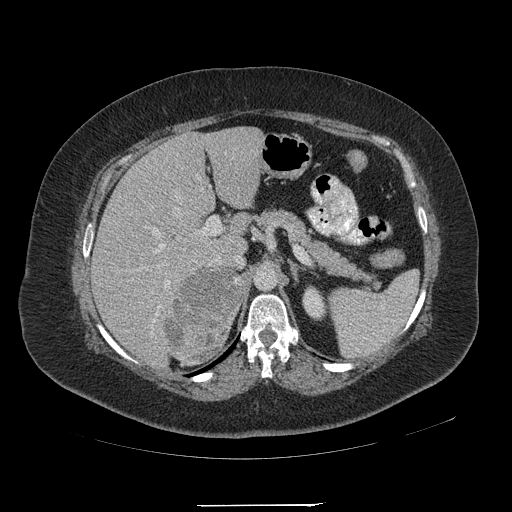
Contrast-enhanced abdominal CT, one axial slice; 120 kVp; soft-tissue window (W 400 / L 40 HU); 512 × 512 image matrix, field of view 453 × 453 mm. Female patient, age 55 years. From the clinical record (not read from this slice): diagnosis: adrenocortical carcinoma; tumour side: right adrenal.
Outlined on this slice (semi-automatically segmented with operator editing):
- mass: box from (x=164, y=267) to (x=243, y=361) px